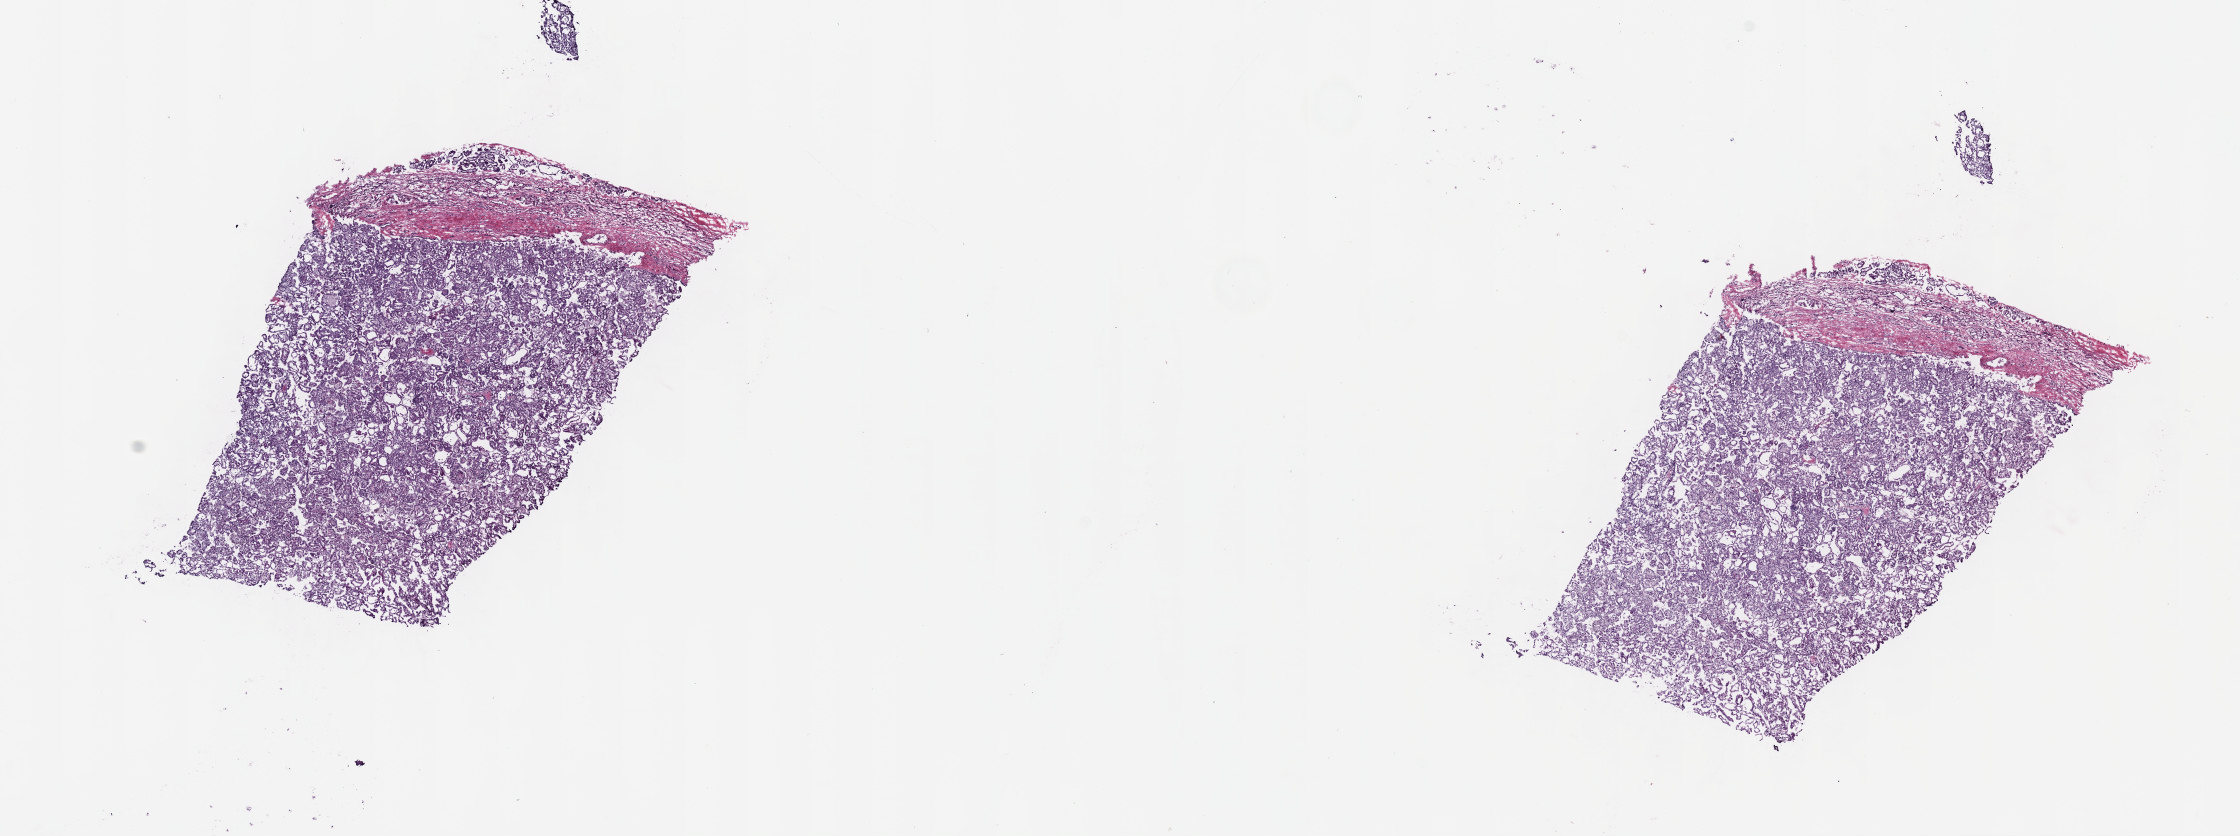
Digitized H&E-stained tissue section (whole slide) — shown as a low-resolution overview of the whole scanned area (about 18.1 x 6.8 mm), frozen section from the top of the tissue portion, kidney, primary tumour sample. Patient: female, age at initial diagnosis 62 years. Slide review estimates, as recorded: tumour cells 100%, tumour nuclei 75%, normal cells 0%, stromal cells 0%, necrosis 0%. Infiltration values recorded for this section: lymphocyte infiltration 3%, monocyte infiltration 3%, neutrophil infiltration 0%.
* histologic diagnosis: Papillary adenocarcinoma, NOS
* laterality: bilateral
* AJCC pathologic stage: I (7th edition)